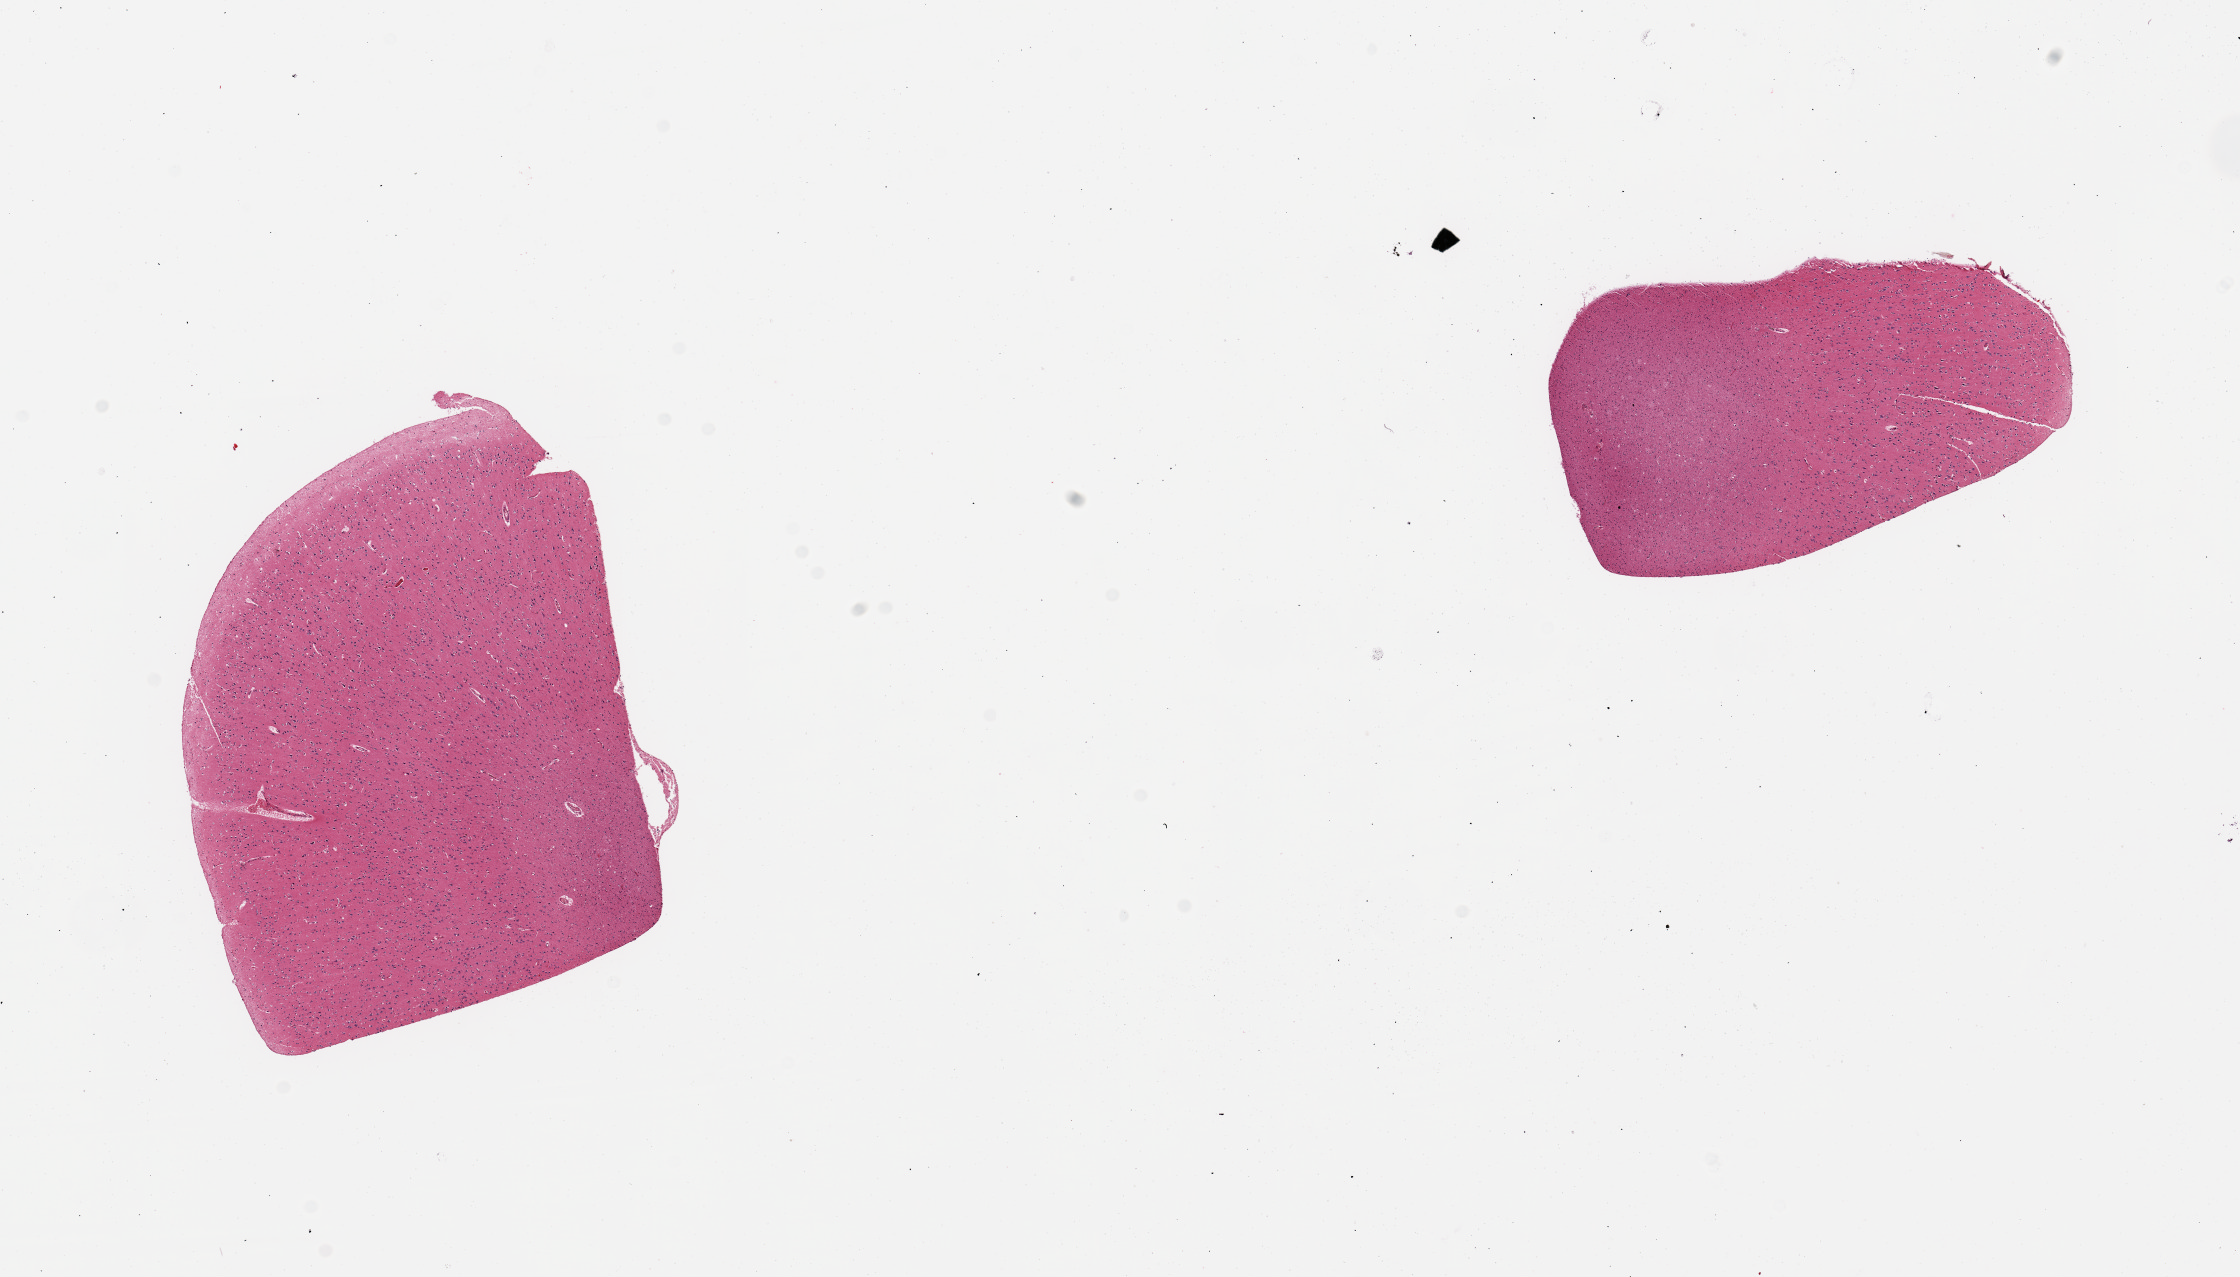
Whole-slide image, haematoxylin and eosin stain — a low-resolution overview of the entire scanned area, about 17.7 x 10.1 mm (slide scanned at 20x). PAXgene-fixed, paraffin-embedded tissue. Sampled site (target tissue): cerebral cortex. Donor tissue sample. Donor: male.
Review note (as recorded): 2 pieces.